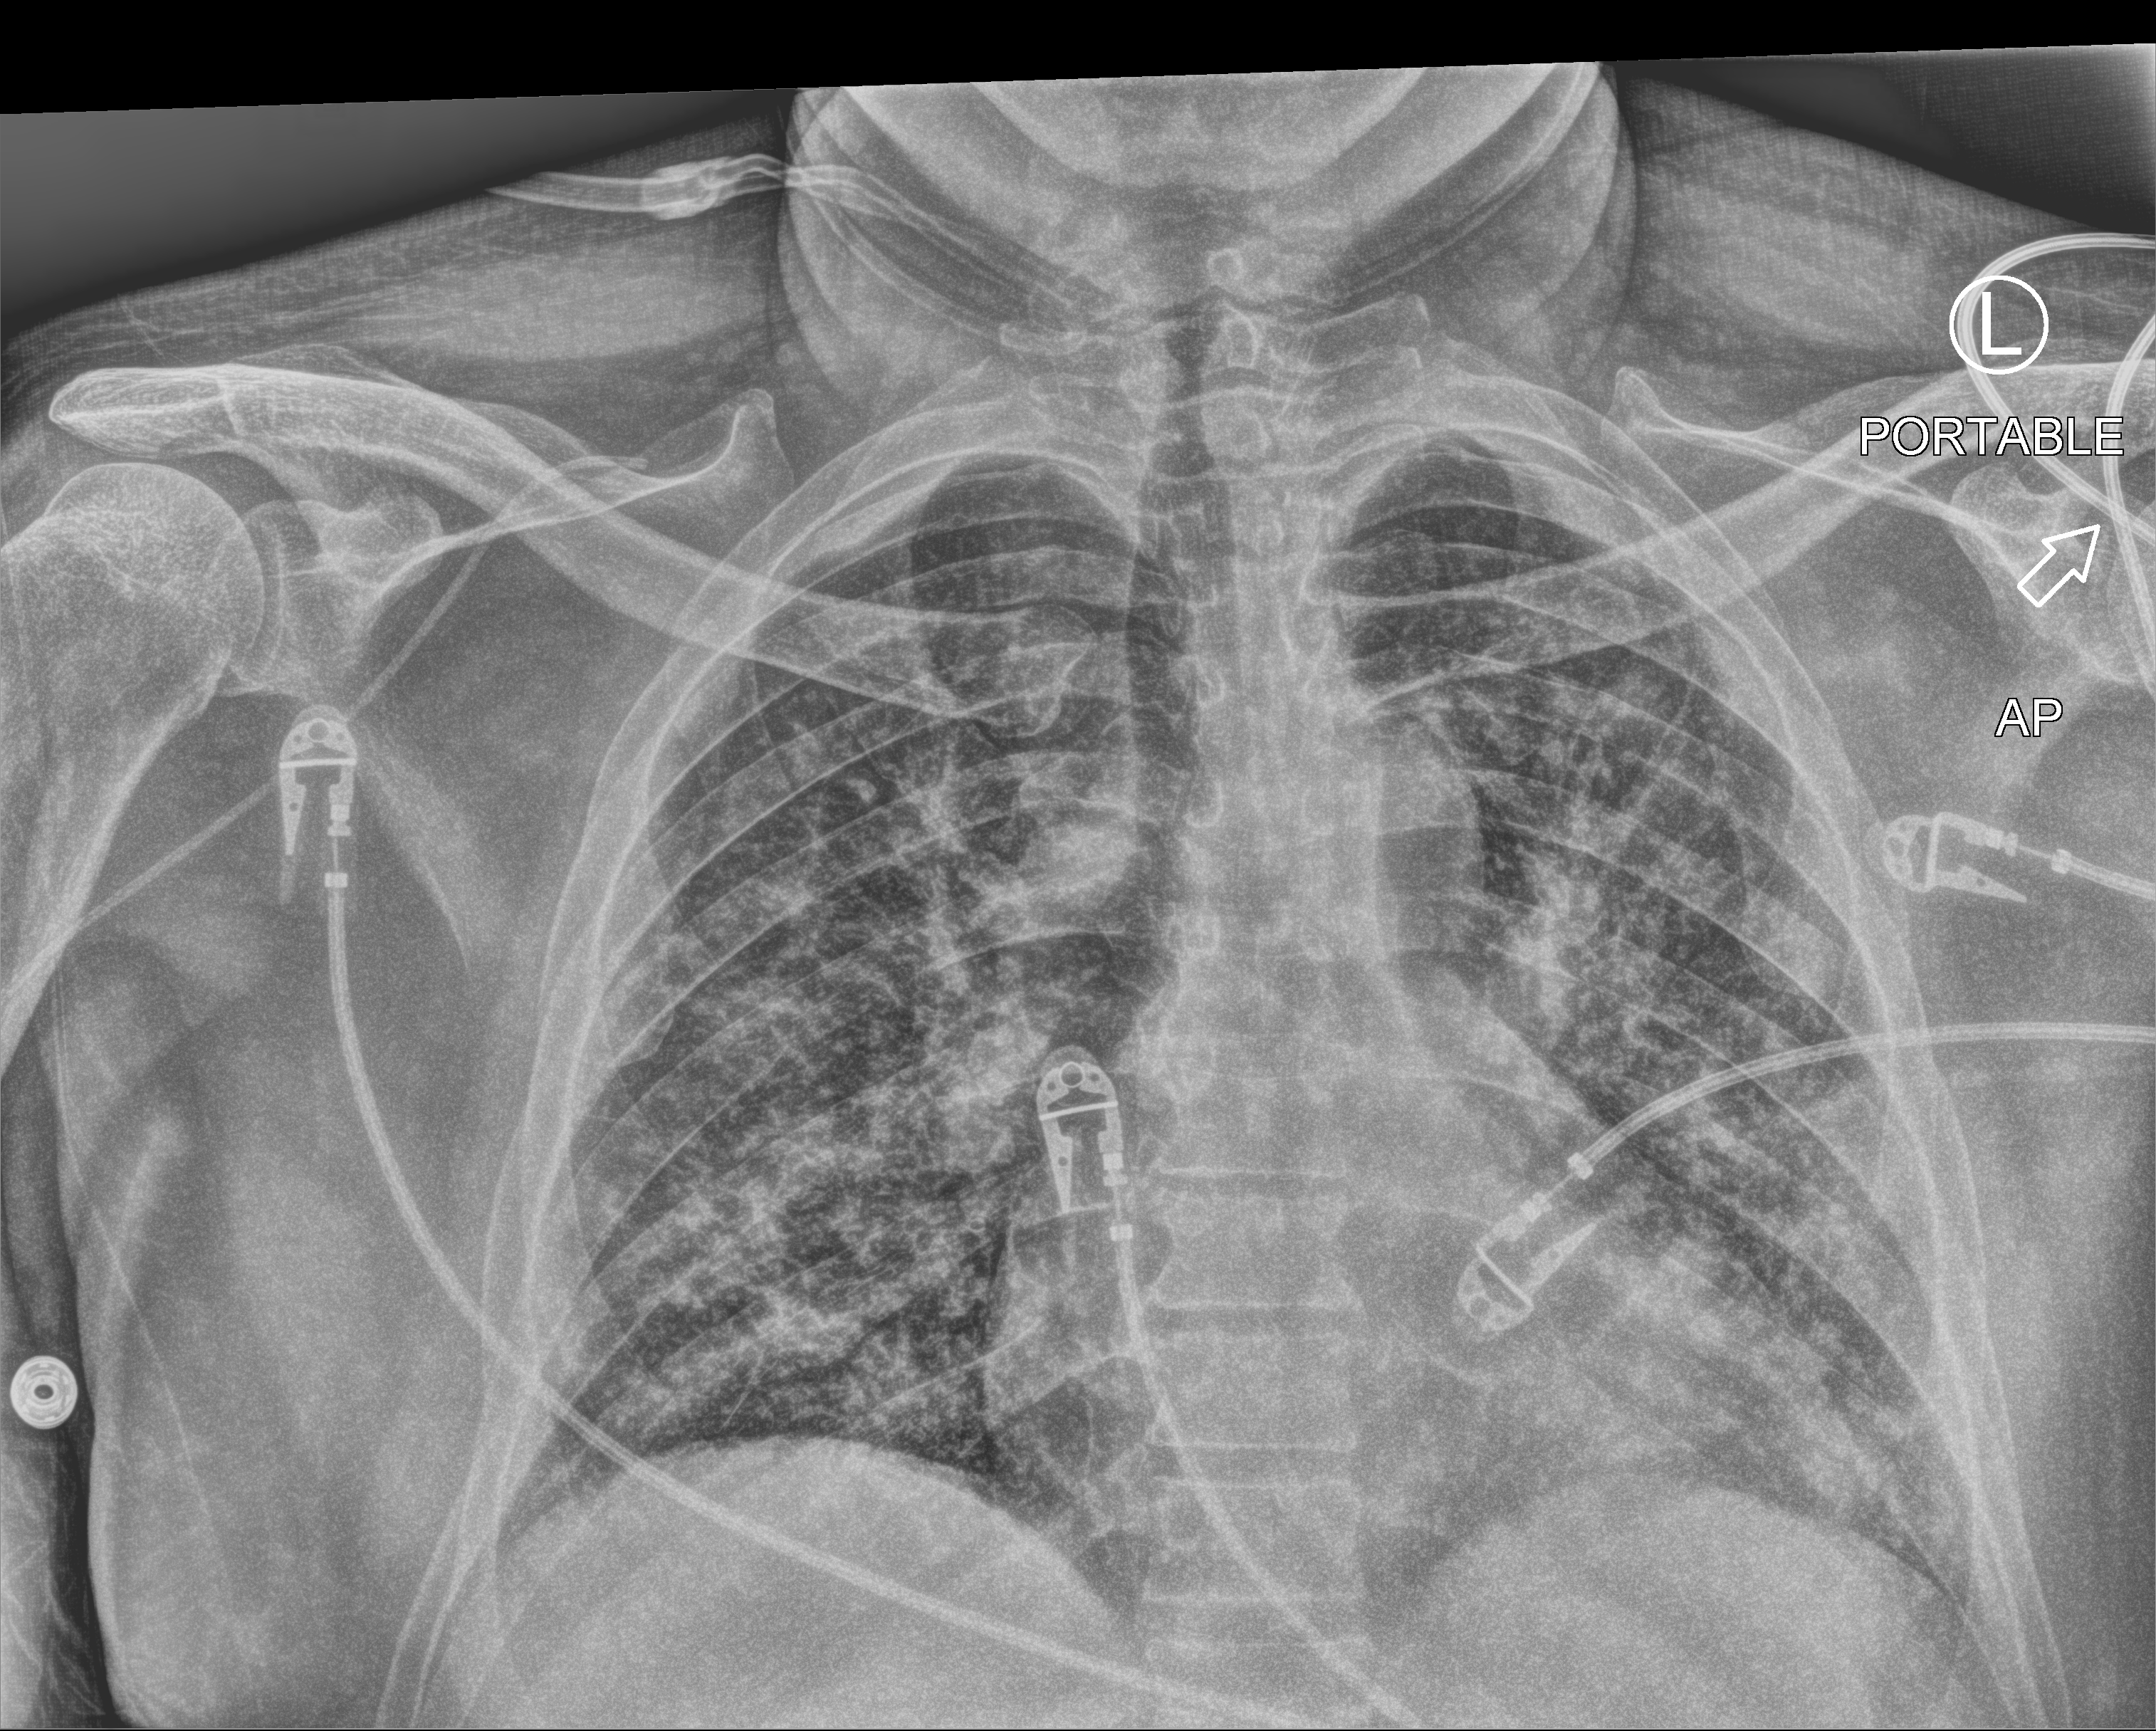
Chest X-ray (portable); anteroposterior (AP) projection. Male patient hospitalised with COVID-19, age 18–59 years.
From the hospital-stay record, not from the radiograph (when in the stay this image was taken is not recorded):
- chronic kidney disease (admission record): no
- mechanically ventilated during this hospital stay: yes